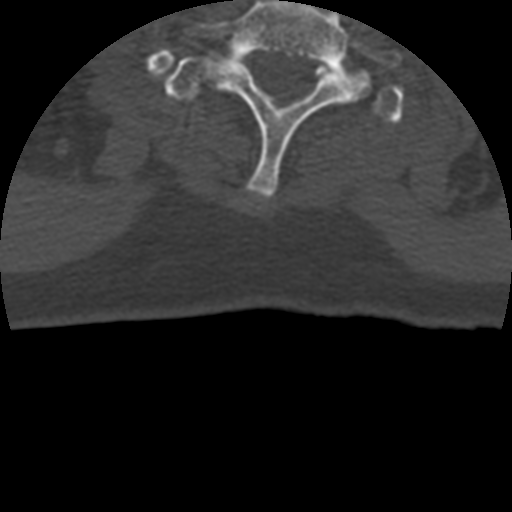
CT including the spine, one axial slice; position 393 of 399 along the scan axis; reconstruction kernel STANDARD; 120 kVp; bone window (W 1800 / L 400 HU); 1.25 mm slice thickness; 512 × 512 image matrix. Patient age 69 years. Case-level facts recorded for this patient, not image findings: primary cancer: prostate.
Annotated regions visible in this slice (semi-automatic segmentation, software-assisted and operator-edited):
- T1 vertebra: bounding box [x1, y1, x2, y2] px = [164, 49, 404, 126]